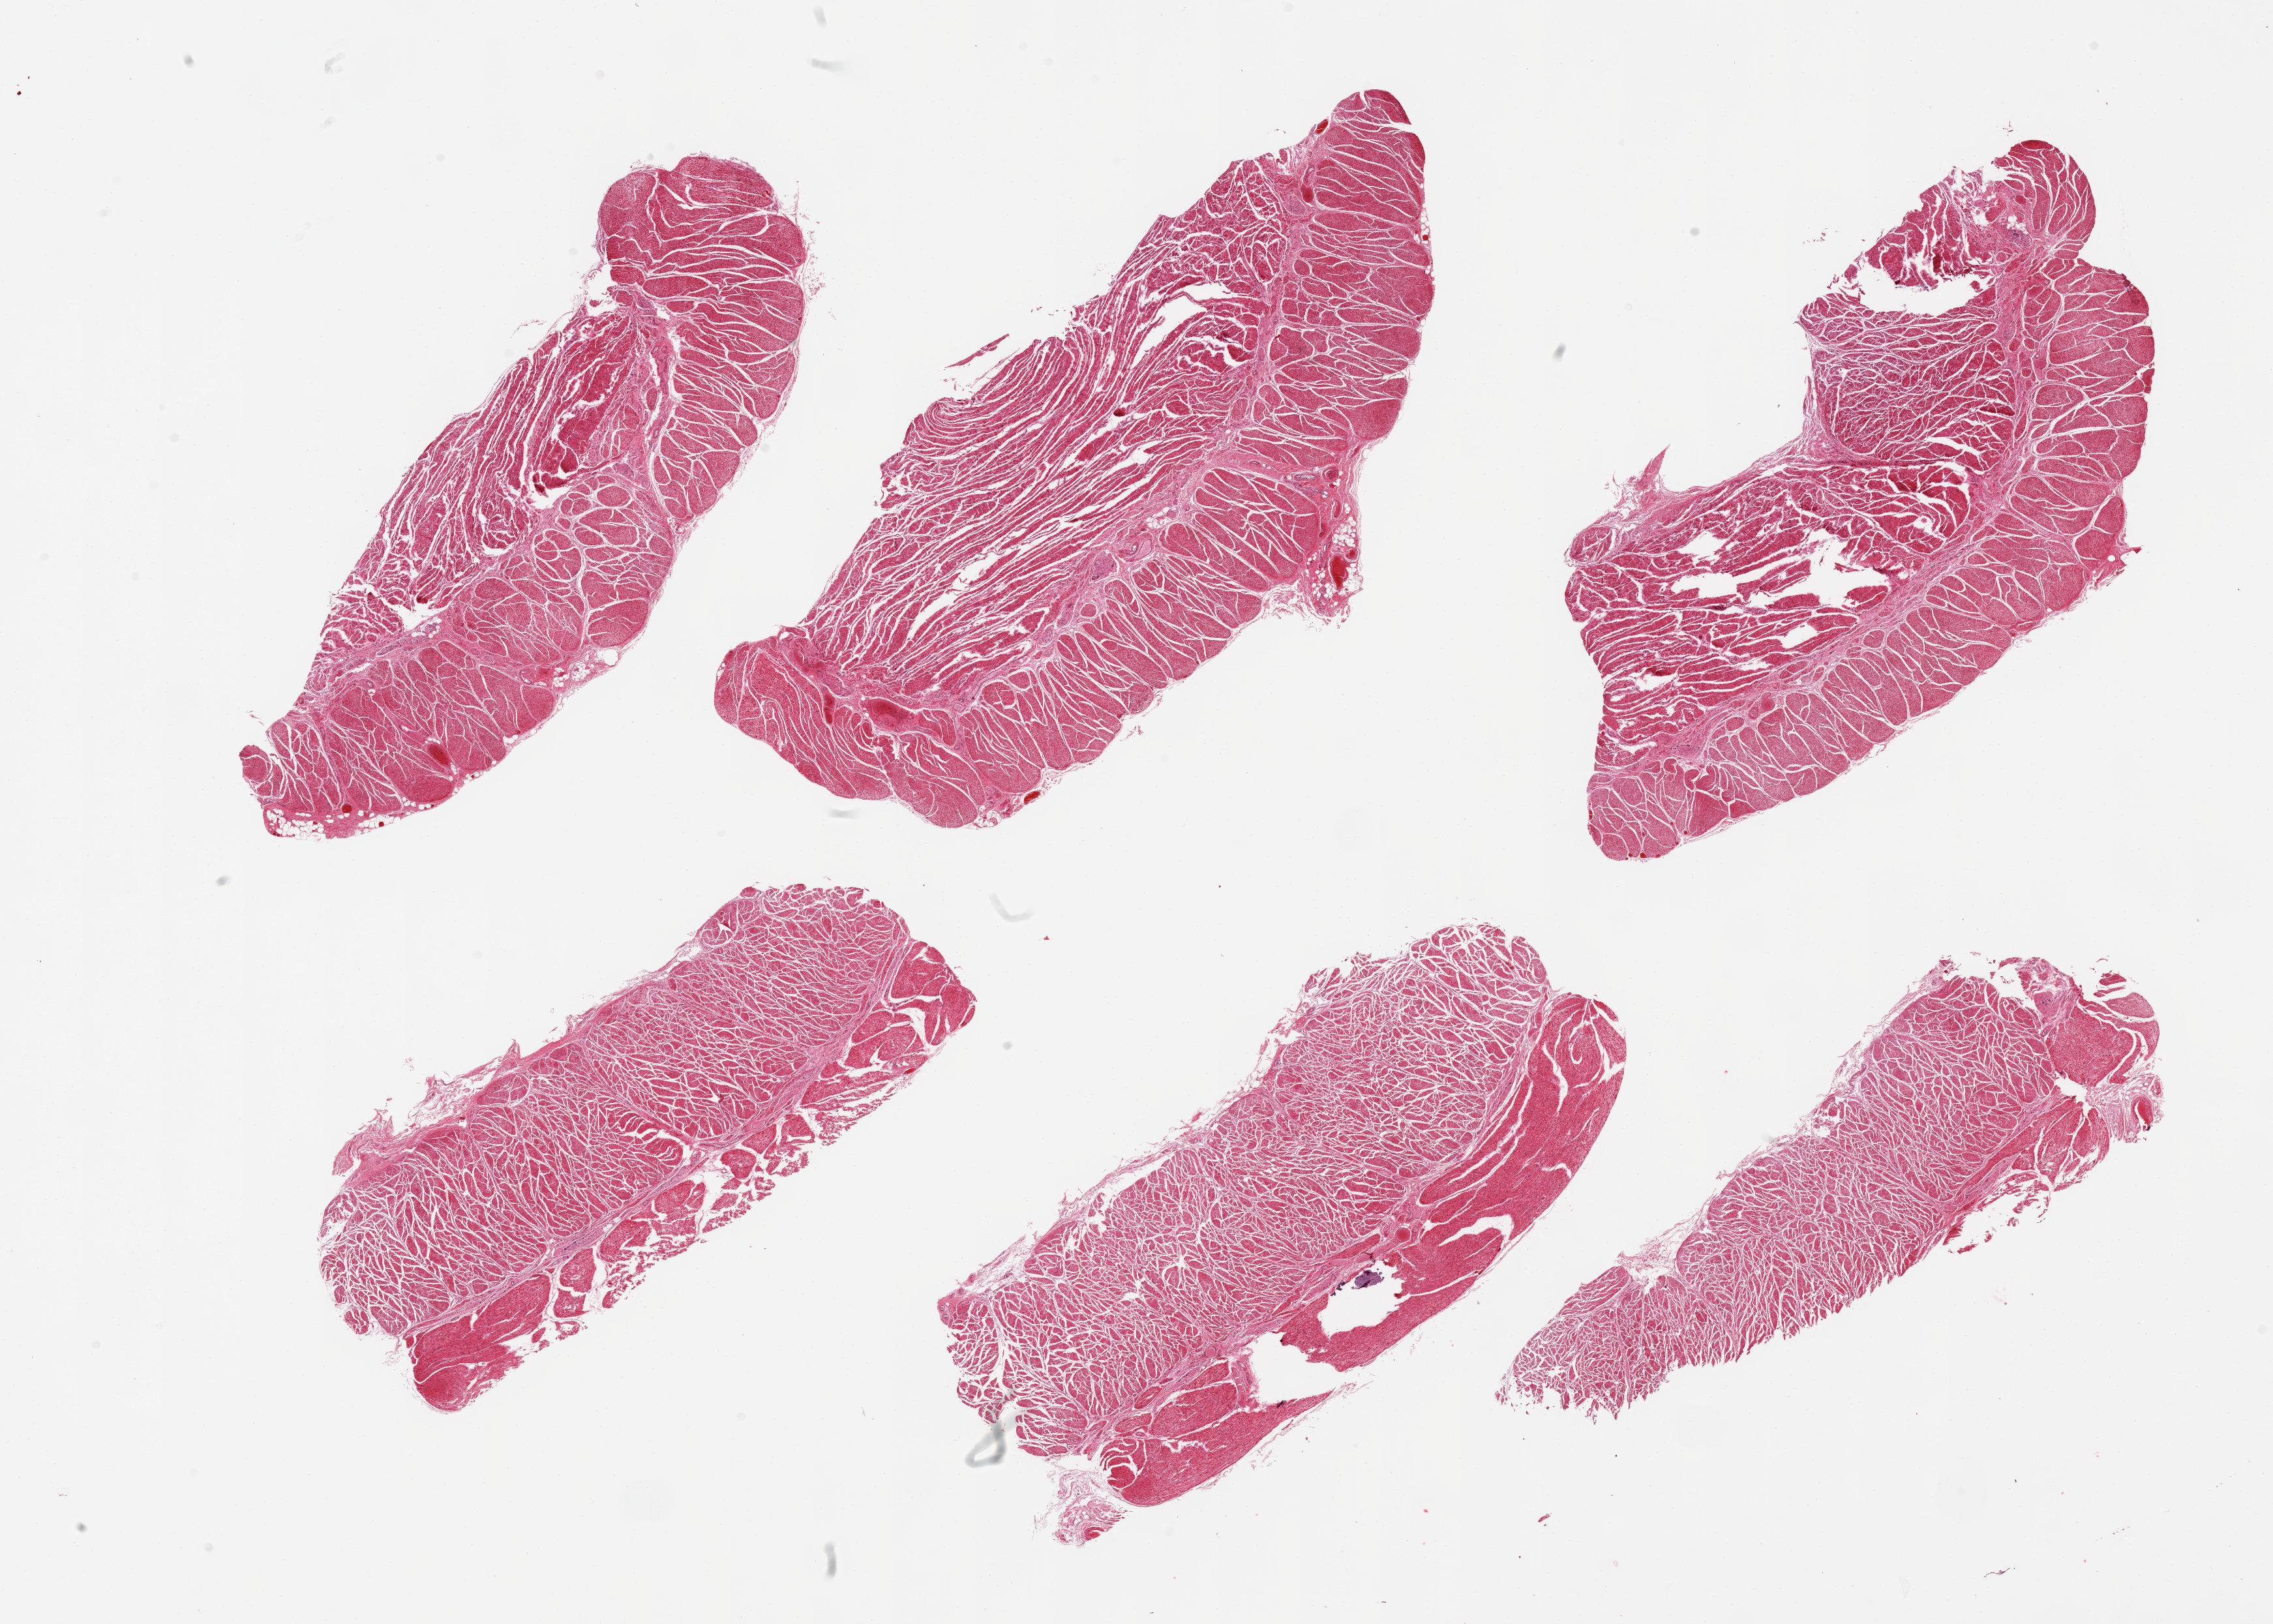
Haematoxylin and eosin whole-slide image, brightfield, shown as a low-resolution overview of the whole scanned area (about 27.6 x 19.7 mm), PAXgene-fixed, paraffin-embedded tissue, target tissue: gastroesophageal junction, tissue donor sample. Male donor.
* pathologist's review note for this sample: 6 pieces; well trimmed muscularis propria